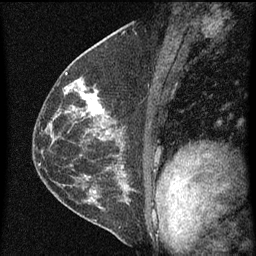
Breast MRI (dynamic contrast-enhanced), one sagittal slice. Position 35 of 60 along the scan axis. Dynamic contrast-enhanced series, image 2 of 4 at this slice position (ordered by acquisition). 1.5 T. TE 4.2 ms, TR 8 ms. 2 mm slice thickness. 256 × 256 image matrix, field of view 180 × 180 mm. Patient: female, 48 years.
Structures marked on this image (semi-automatically segmented with operator editing):
- analysis volume of interest (the breast-tissue region the enhancement analysis was run in; not a lesion): bounding box [x1, y1, x2, y2] px = [73, 82, 115, 139]
- tumour enhancement mask (voxels above the 70 % enhancement threshold inside the analysis volume of interest): [73, 84, 108, 139]